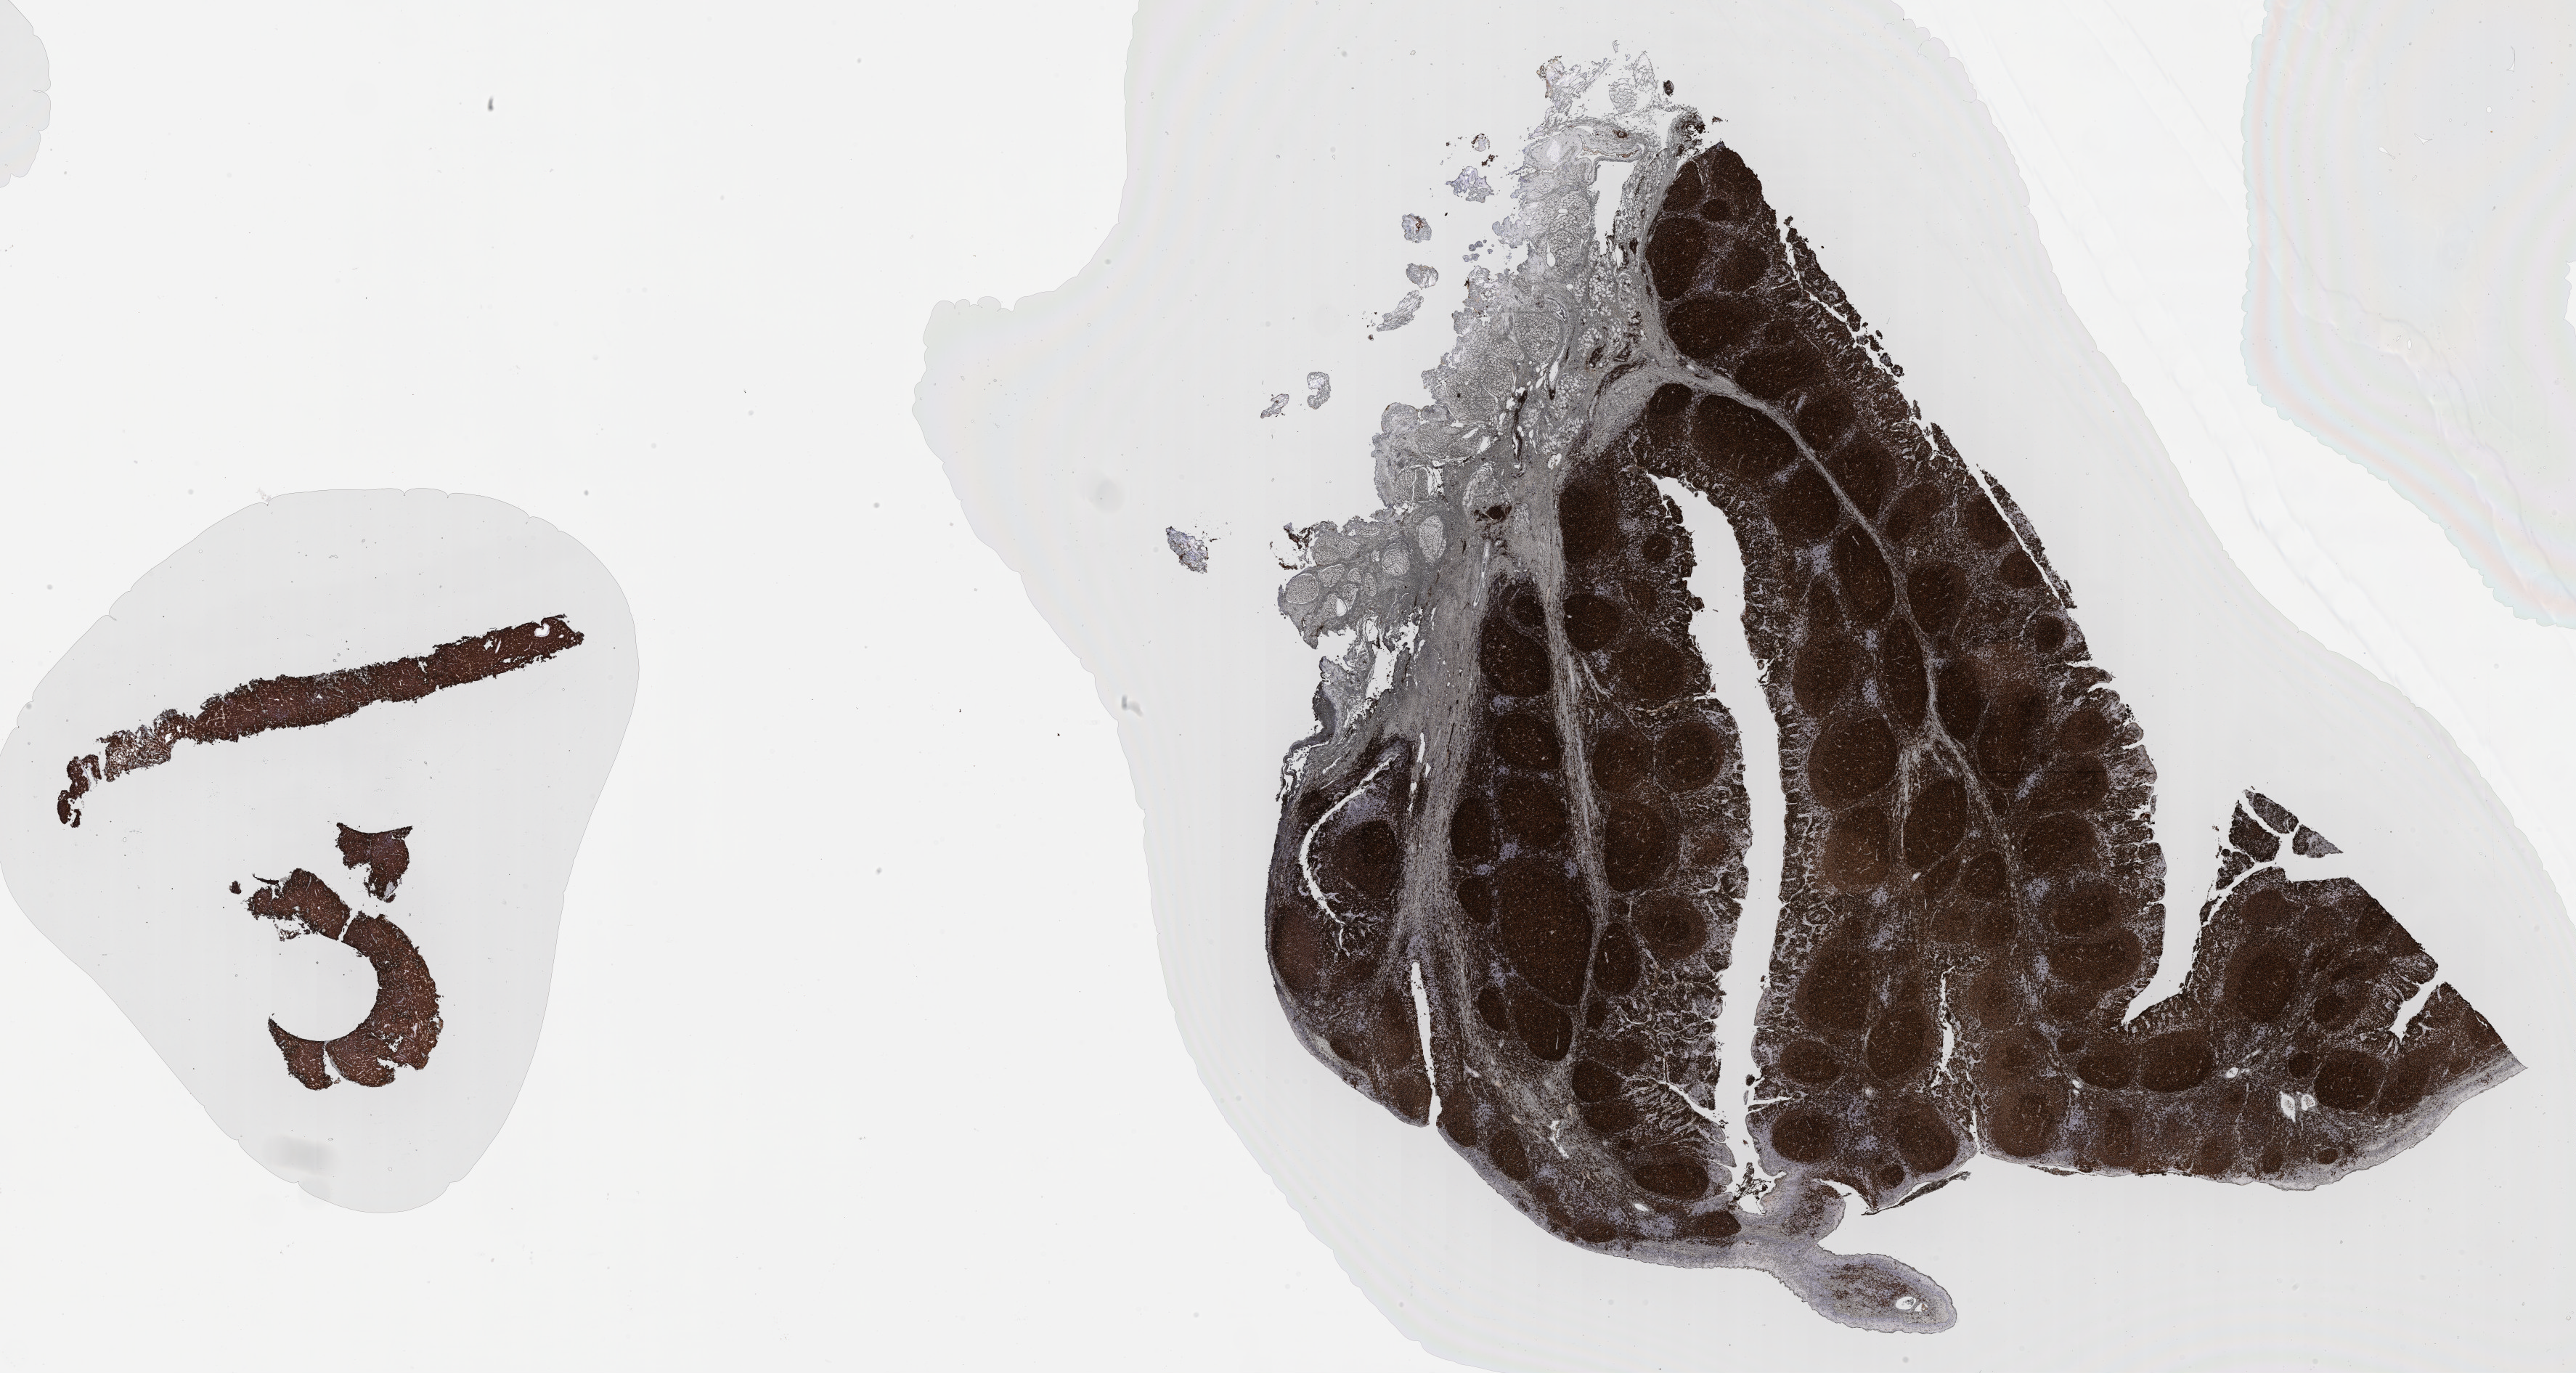
Immunohistochemistry (IHC) whole-slide image stained for CD20, shown as a low-resolution overview of the whole scanned area (about 28.7 x 15.3 mm). Tumor tissue. Anatomic site: ovary. Patient female; aged 10.
- diagnosis: Burkitt lymphoma, NOS